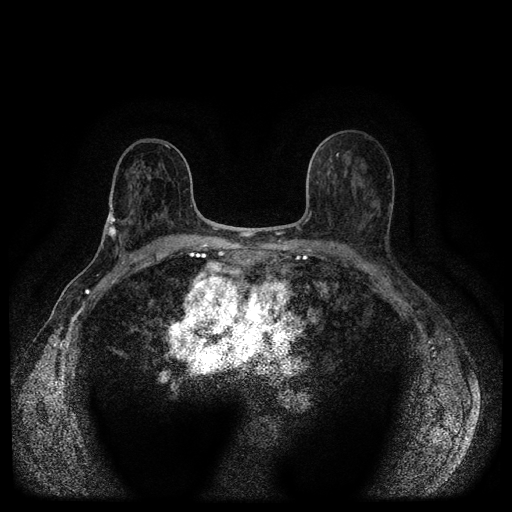
Breast MRI (dynamic contrast-enhanced, multi-phase), one axial slice; slice 62 of 116 in the series (ordered by position); dynamic contrast-enhanced series, time point 2 of 5 at this slice position (early post-contrast); 1.5 T; TE 2.7 ms, TR 5.4 ms; 512 × 512 image matrix, field of view 340 × 340 mm. Patient: female, 75 years.
Structures marked on this image (semi-automatic segmentation, software-assisted and operator-edited):
- breast lesion (labelled 'tumour' in the annotation; benign lesions carry a separate 'benign' label): box from (x=104, y=211) to (x=118, y=240) px